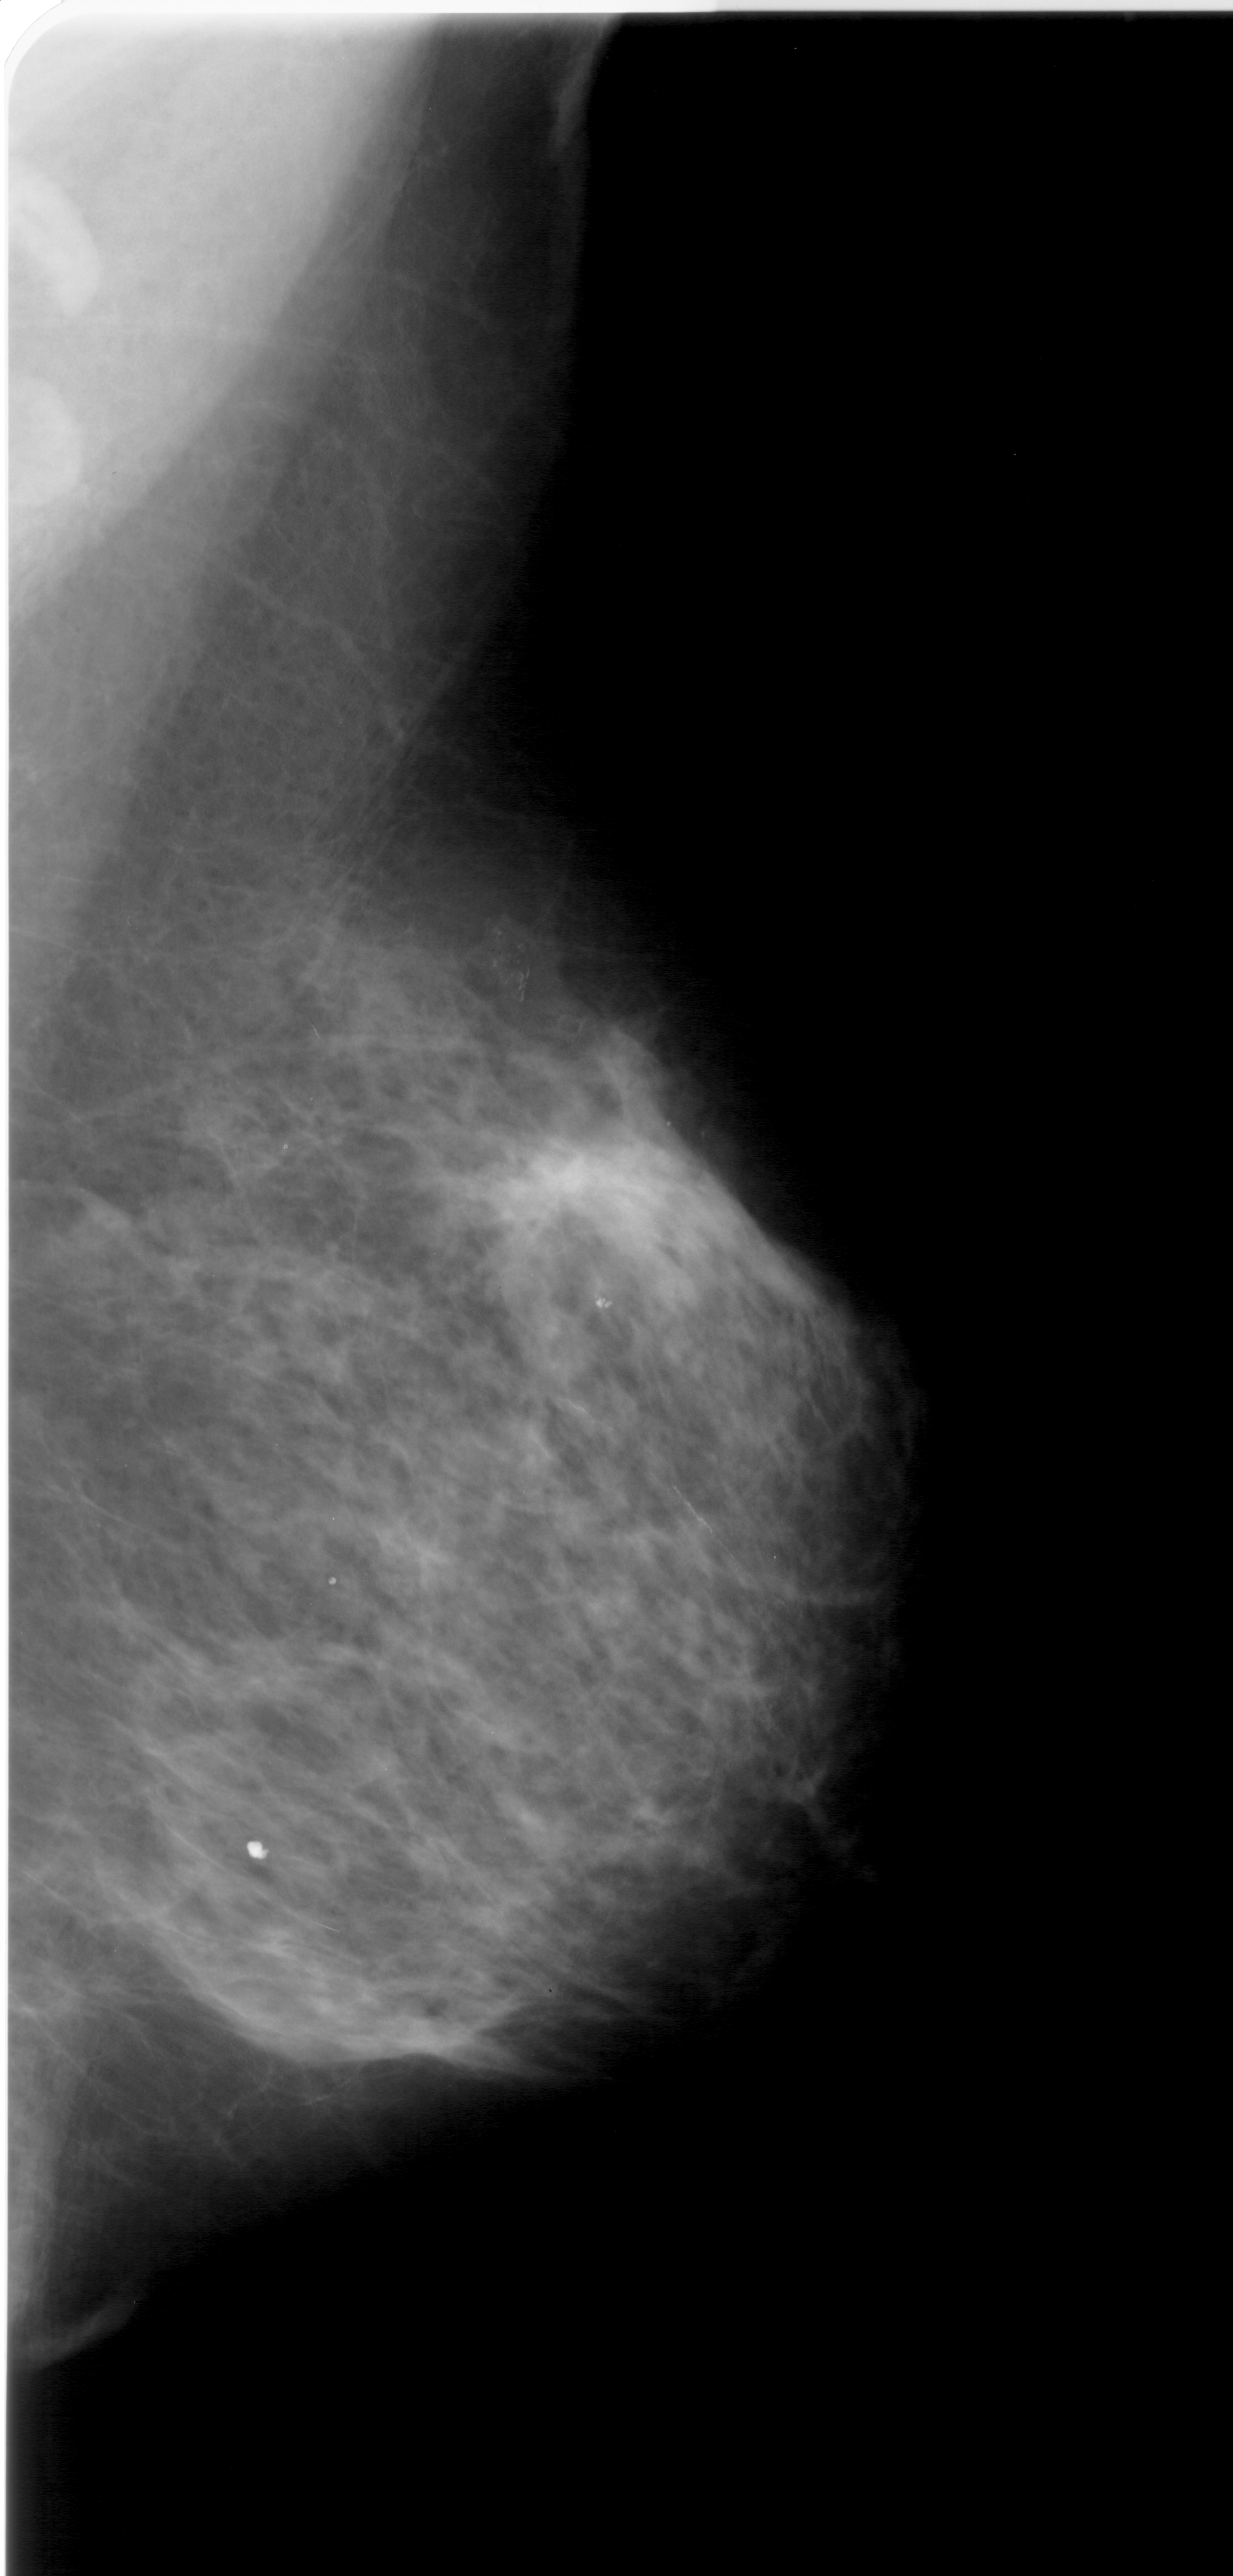
Mammogram (digitized film), right breast, MLO view.
Abnormality record for this image: calcifications, morphology pleomorphic, distribution clustered; BI-RADS assessment category 4; pathology (as recorded): benign.